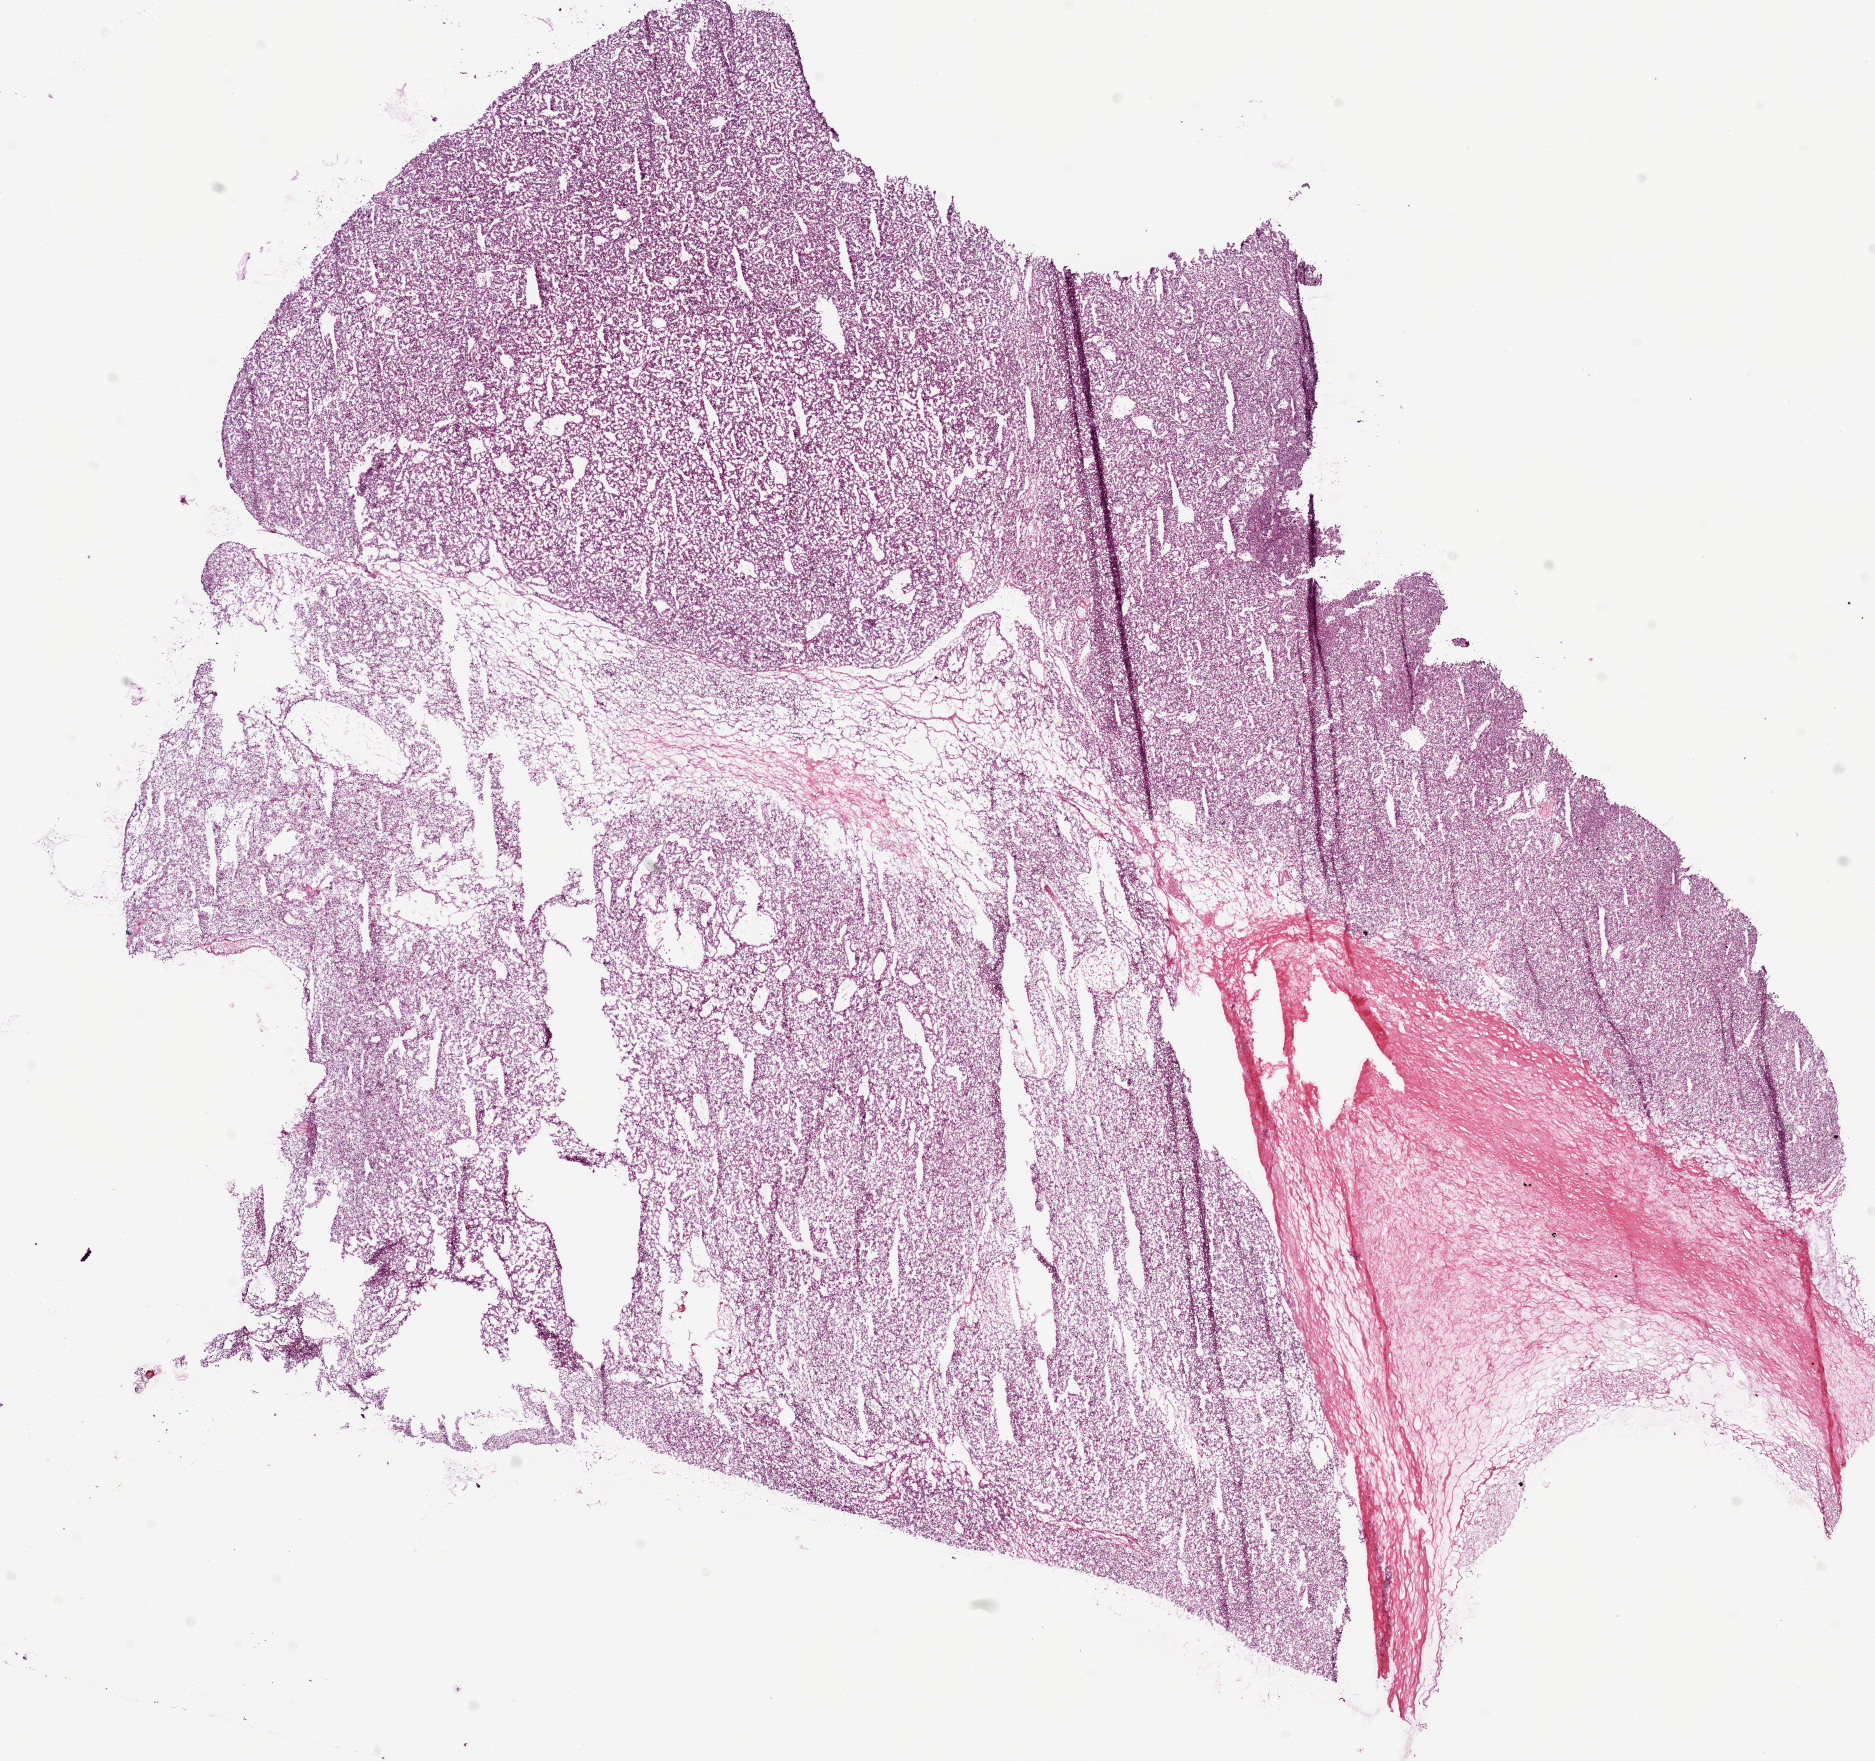
Whole-slide histology image, H&E — a low-resolution overview of the entire scanned area, about 15.0 x 14.1 mm (slide scanned at 20x); frozen section from the bottom of the tissue portion; primary tumour sample from the kidney. Female patient; age at initial diagnosis 82 years. Histologic grade: G2 (moderately differentiated). Composition of this section per pathologist review: tumour cells 80%, tumour nuclei 90%, normal cells 0%, stromal cells 20%, necrosis 0%.
- AJCC pathologic stage: I
- pathologic diagnosis: Clear cell adenocarcinoma, NOS
- laterality: left